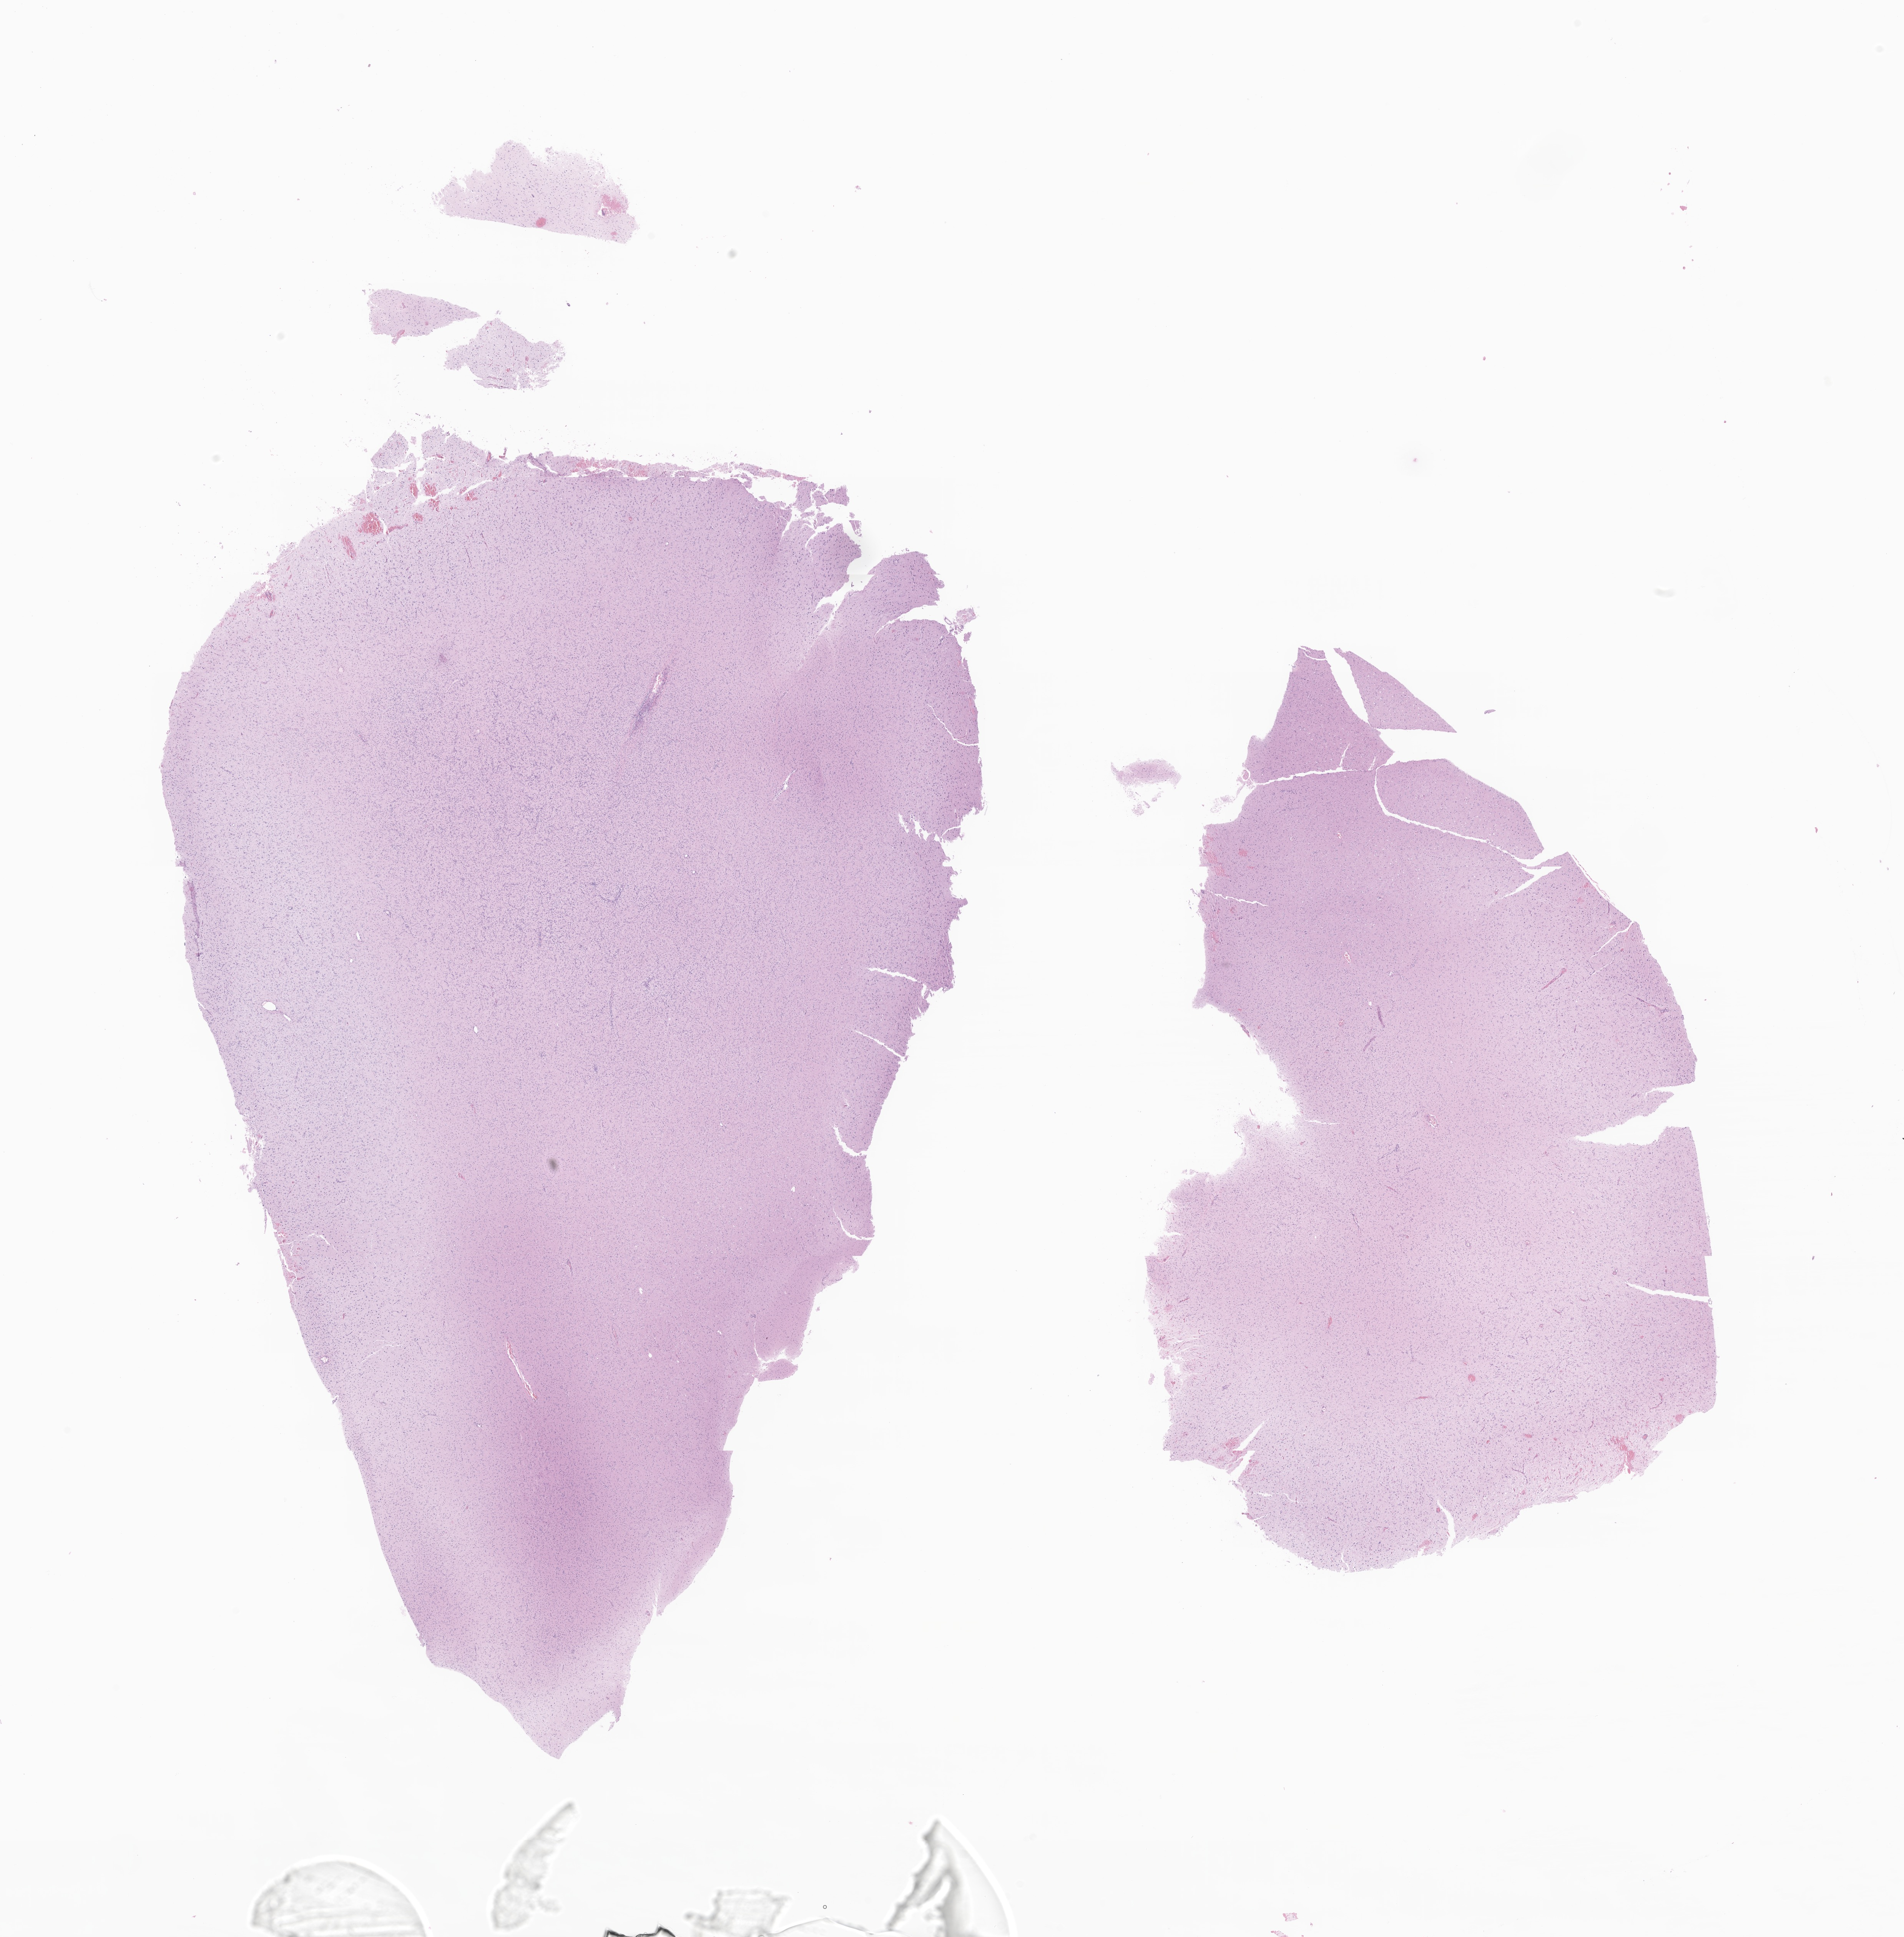
Whole-slide image, hematoxylin and eosin (H&E) stain of tumor tissue from the parietal lobe, low-resolution overview of the scanned area, about 20.9 x 21.2 mm. FFPE section. Patient: female, age 81 months (6 years 9 months).
• recorded diagnosis: Dysembryoplastic neuroepithelial tumor